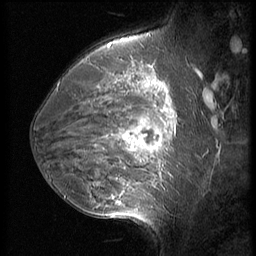
Breast MRI (dynamic contrast-enhanced), one sagittal slice; position 39 of 56 along the scan axis; 3 images stored at this slice position (order not interpretable as contrast timing); 1.5 T; TE 4.2 ms, TR 9 ms; 2.5 mm slice thickness; 256 × 256 image matrix, field of view 180 × 180 mm. Patient: female, 35 years. From the clinical record (not read from this slice): setting: breast cancer imaged before/during neoadjuvant chemotherapy; receptor status: HR-positive, HER2-negative.
Outlined on this slice (semi-automatically segmented with operator editing):
- analysis volume of interest (the breast-tissue region the enhancement analysis was run in; not a lesion): box from (x=63, y=60) to (x=190, y=218) px
- tumour enhancement mask (voxels above the 140 % enhancement threshold inside the analysis volume of interest): (x=104, y=83)–(x=172, y=205)